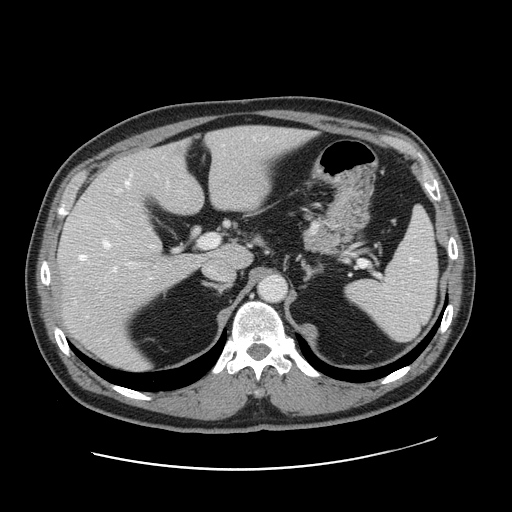
Contrast-enhanced abdominal CT, one axial slice; 120 kVp; intravenous contrast given; soft-tissue window (W 400 / L 40 HU); 2.5 mm slice thickness; 512 × 512 image matrix, field of view 403 × 403 mm. Male patient, age 63 years. From the clinical record (not read from this slice): diagnosis: colorectal cancer liver metastases, imaged before liver resection; multiple liver metastases: yes.
Annotated regions visible in this slice (manually delineated by an expert):
- hepatic veins: bounding box <80,181,128,270> (left, top, right, bottom; pixels)
- liver: <59,127,305,371>
- planned liver remnant (the part of the liver to remain after resection): <122,126,306,266>
- portal vein (with intrahepatic branches): <110,219,220,265>